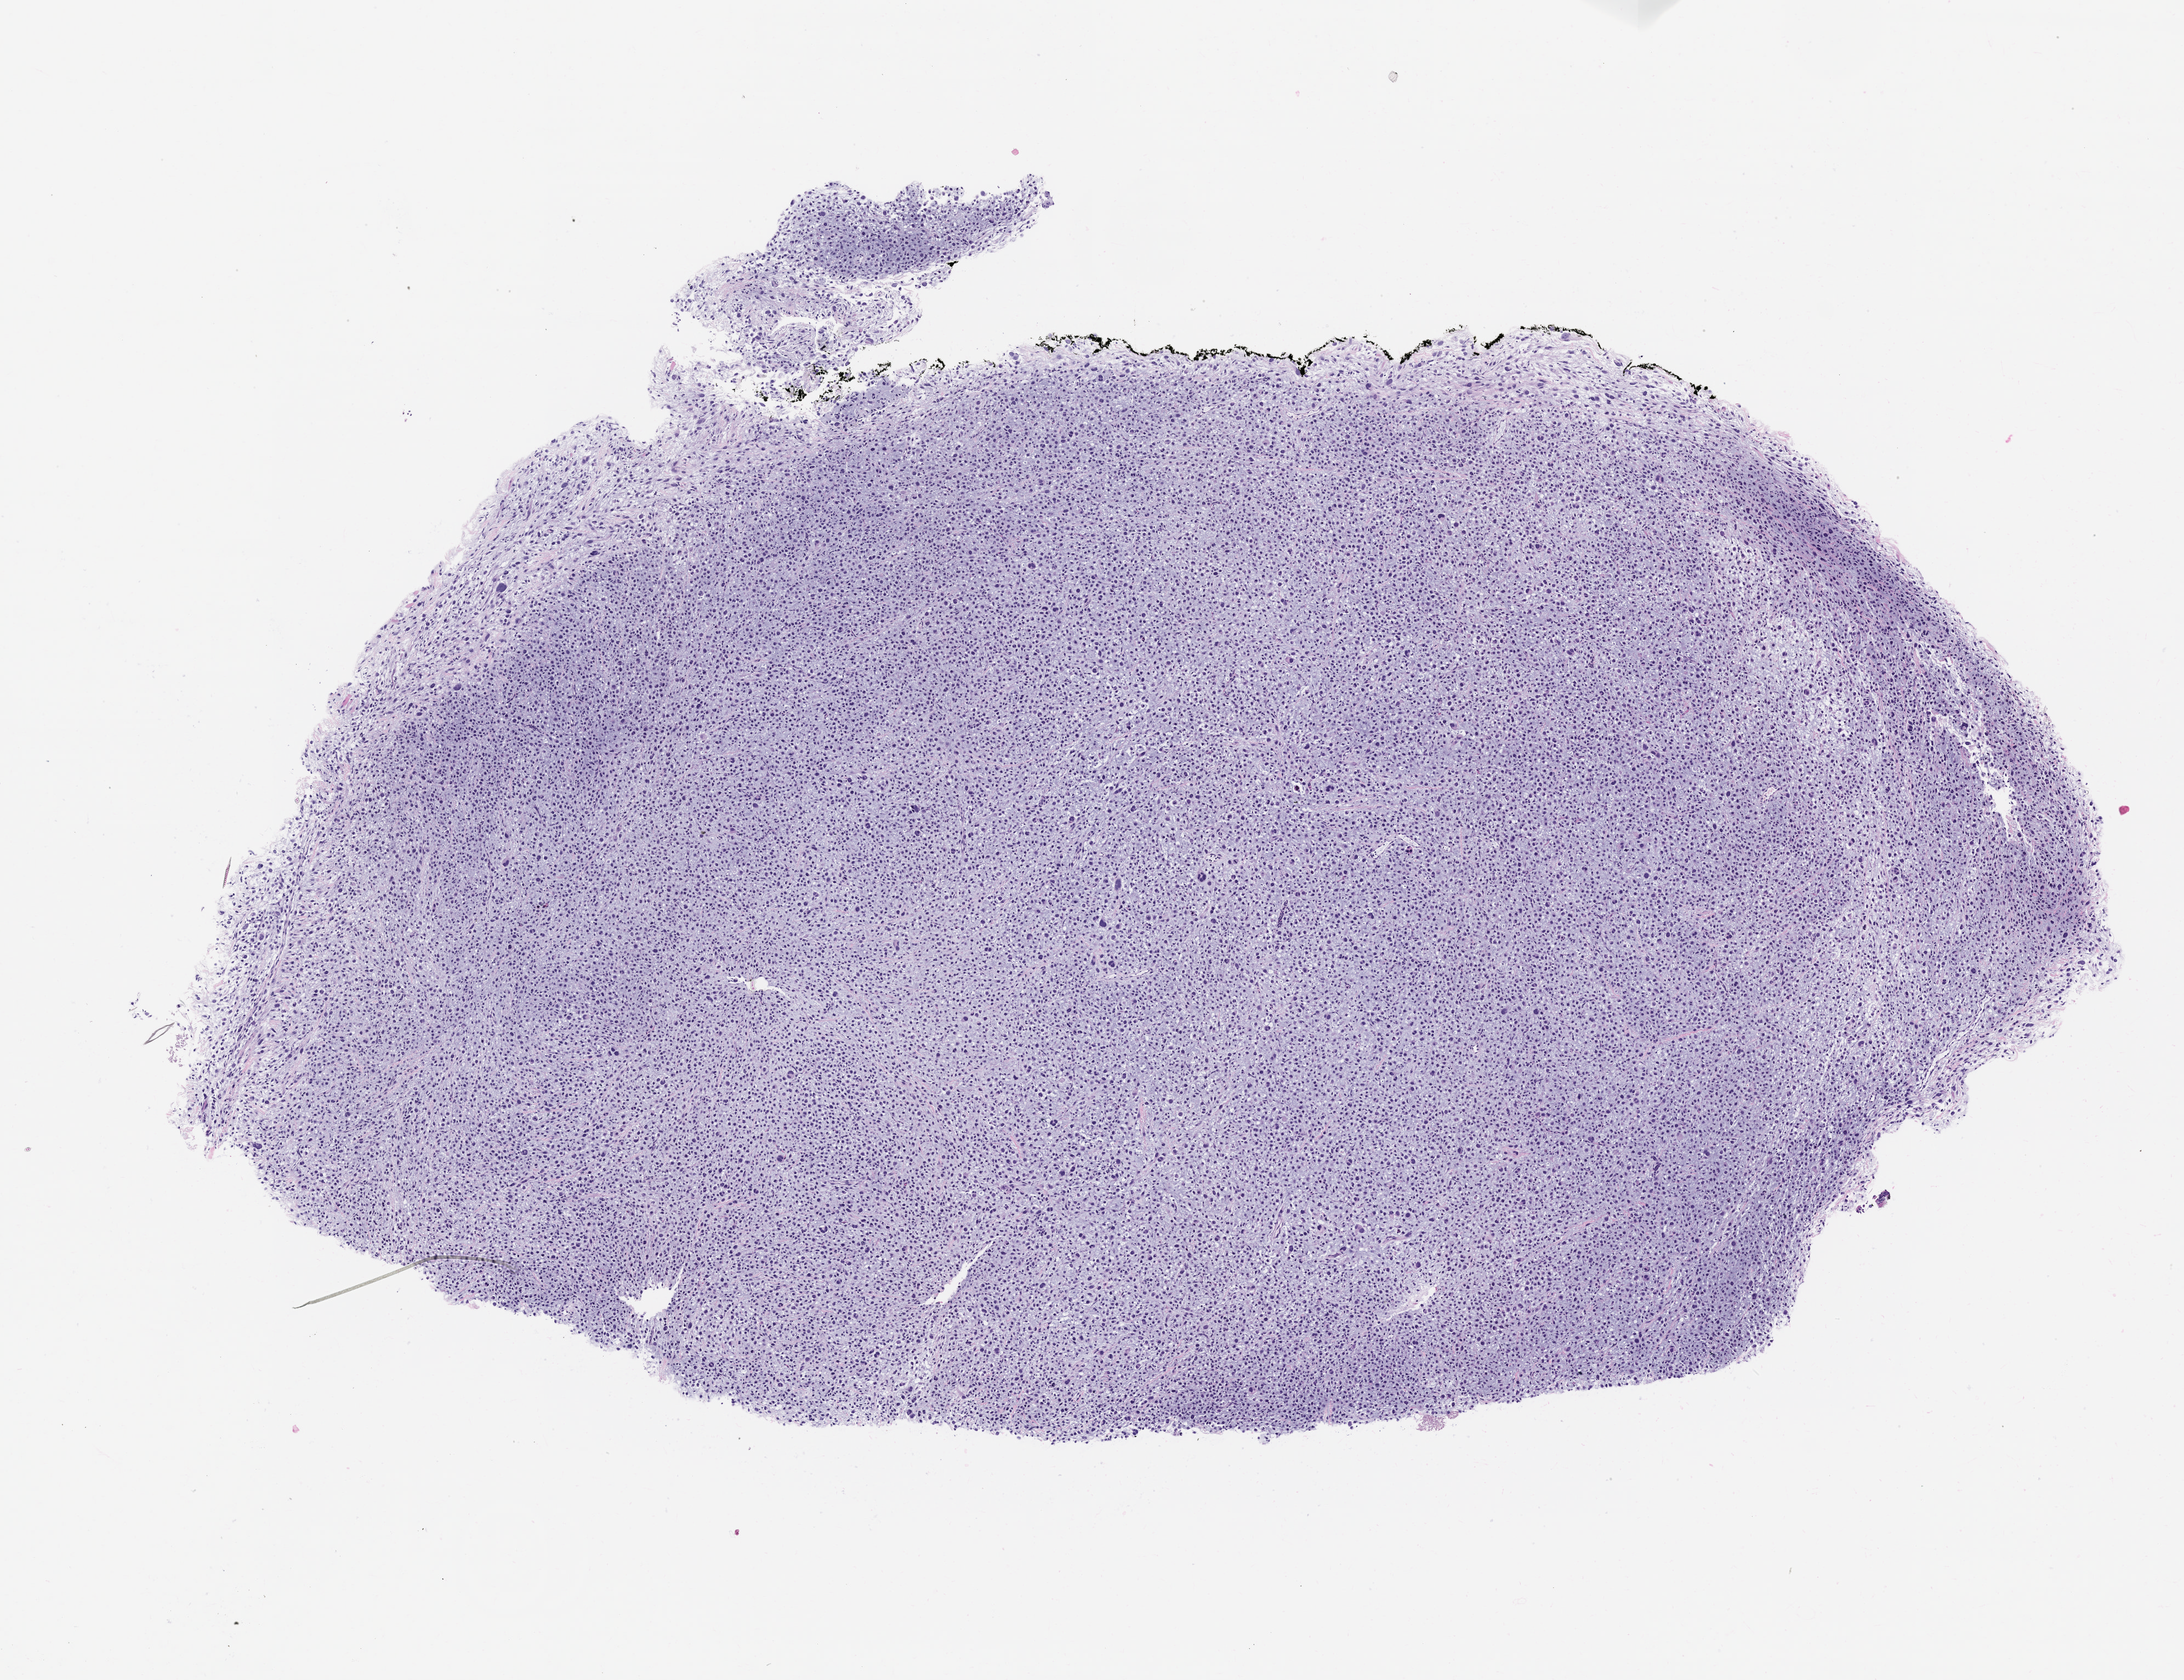
Haematoxylin and eosin whole-slide image of a patient-derived xenograft (PDX) tumor grown in a mouse, passage 1 — low-resolution overview of the scanned area, about 8.0 x 6.2 mm; formalin-fixed paraffin-embedded section; tumor site category: musculoskeletal.
Originating patient diagnosis: Myxofibrosarcoma.